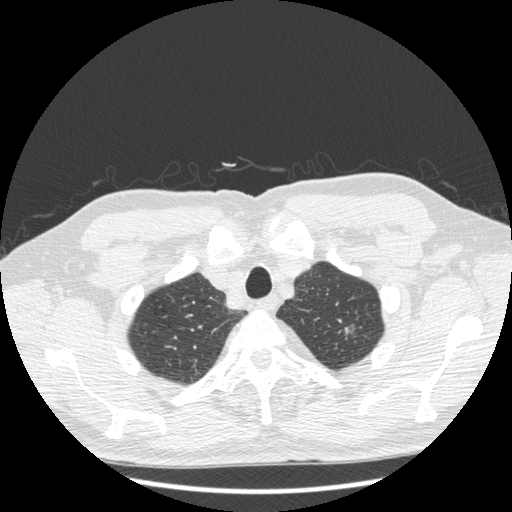
Low-dose screening chest CT, one axial slice; position 189 of 223 along the scan axis; reconstruction kernel STANDARD; lung window (W 1500 / L -600 HU); 1.25 mm slice thickness; 512 × 512 image matrix, field of view 380 × 380 mm.
Outlined on this slice (manually delineated by an expert):
- lesion 1 (tumor, upper lobe of left lung): box from (x=345, y=327) to (x=351, y=340) px